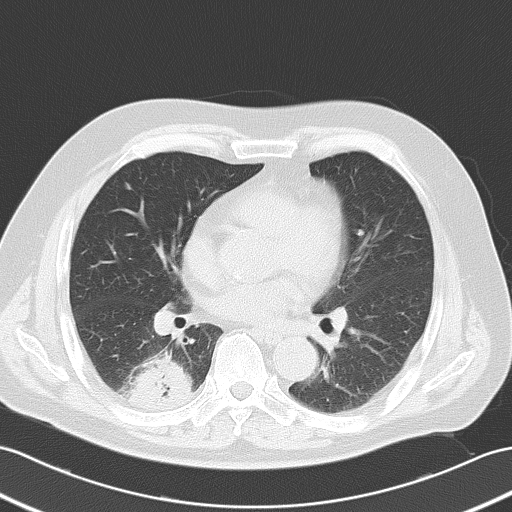
Chest CT, one axial slice. Slice 20 of 52 in the series (ordered by position). 120 kVp. Lung window (W 1500 / L -600 HU). 5 mm slice thickness. 512 × 512 image matrix. Male patient, age 70 years. Case-level facts recorded for this patient, not image findings: clinical TNM (as recorded): T2 N0 M0.
Annotated regions visible in this slice (bounding box drawn by a radiologist):
- lung tumour (recorded histology: adenocarcinoma): box from (x=126, y=355) to (x=197, y=413) px